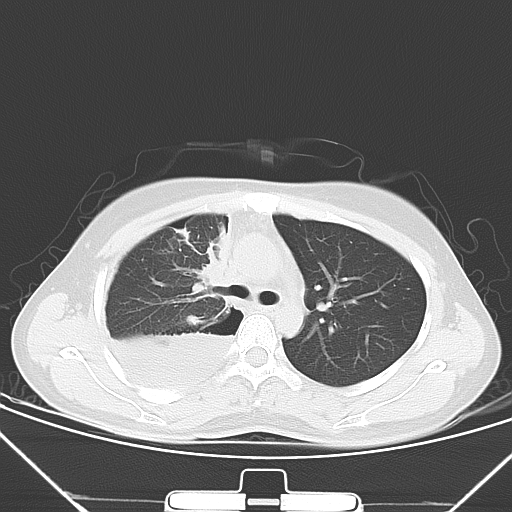
Chest CT, one axial slice; 120 kVp; lung window (W 1500 / L -600 HU); 5 mm slice thickness; 512 × 512 image matrix, field of view 343 × 343 mm. Patient: female, 28 years. From the clinical record (not read from this slice): clinical TNM (as recorded): T2 N0 M1a.
Annotated regions visible in this slice (bounding box drawn by a radiologist):
- lung tumour (recorded histology: adenocarcinoma): bounding box [x1, y1, x2, y2] px = [192, 231, 228, 302]